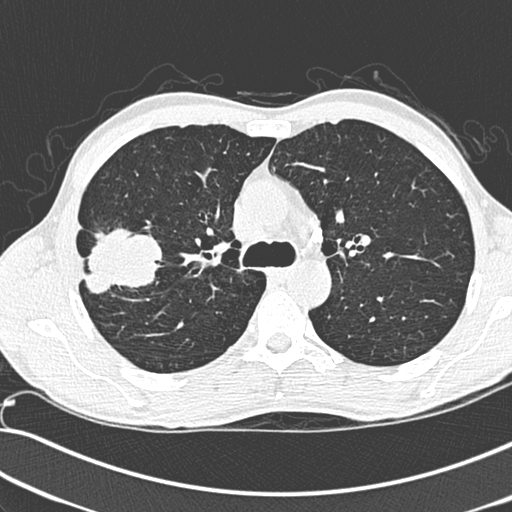
Low-dose screening chest CT, one axial slice. Slice 202 of 281 in the series (ordered by position). 120 kVp. Lung window (W 1500 / L -600 HU). 1.3 mm slice thickness. 512 × 512 image matrix, field of view 341 × 341 mm.
Annotated regions visible in this slice (expert manual segmentation):
- lesion 1 (tumor, upper lobe of right lung): box from (x=83, y=225) to (x=166, y=295) px